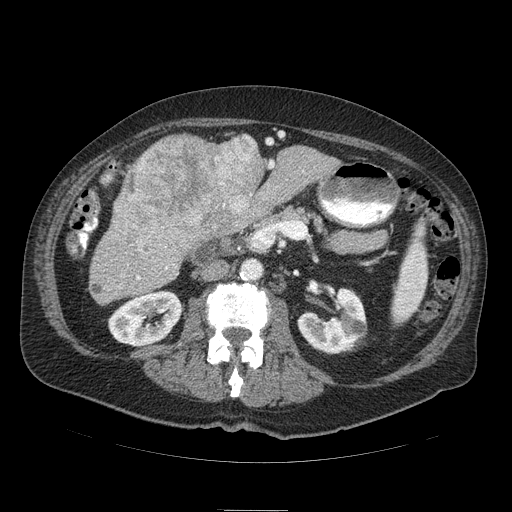
Contrast-enhanced abdominal CT (liver protocol), one axial slice. Position 31 of 103 along the scan axis. Soft-tissue window (W 400 / L 40 HU). 2.5 mm slice thickness. 512 × 512 image matrix, field of view 440 × 440 mm. From the clinical record (not read from this slice): diagnosis: hepatocellular carcinoma (patient treated with transarterial chemoembolisation; whether this scan precedes or follows treatment is not stated here); TNM stage (as recorded): Stage-IIIA; Child-Pugh class: B; tumour differentiation: well differentiated; tumour nodularity: multinodular.
Outlined on this slice (semi-automatically segmented with operator editing):
- liver parenchyma outside the tumour (the mass and vessels are separate outlines, so this box may not span the whole liver): box from (x=90, y=135) to (x=339, y=298) px
- mass: (x=117, y=134)–(x=265, y=257)
- liver vessels: (x=137, y=161)–(x=274, y=280)